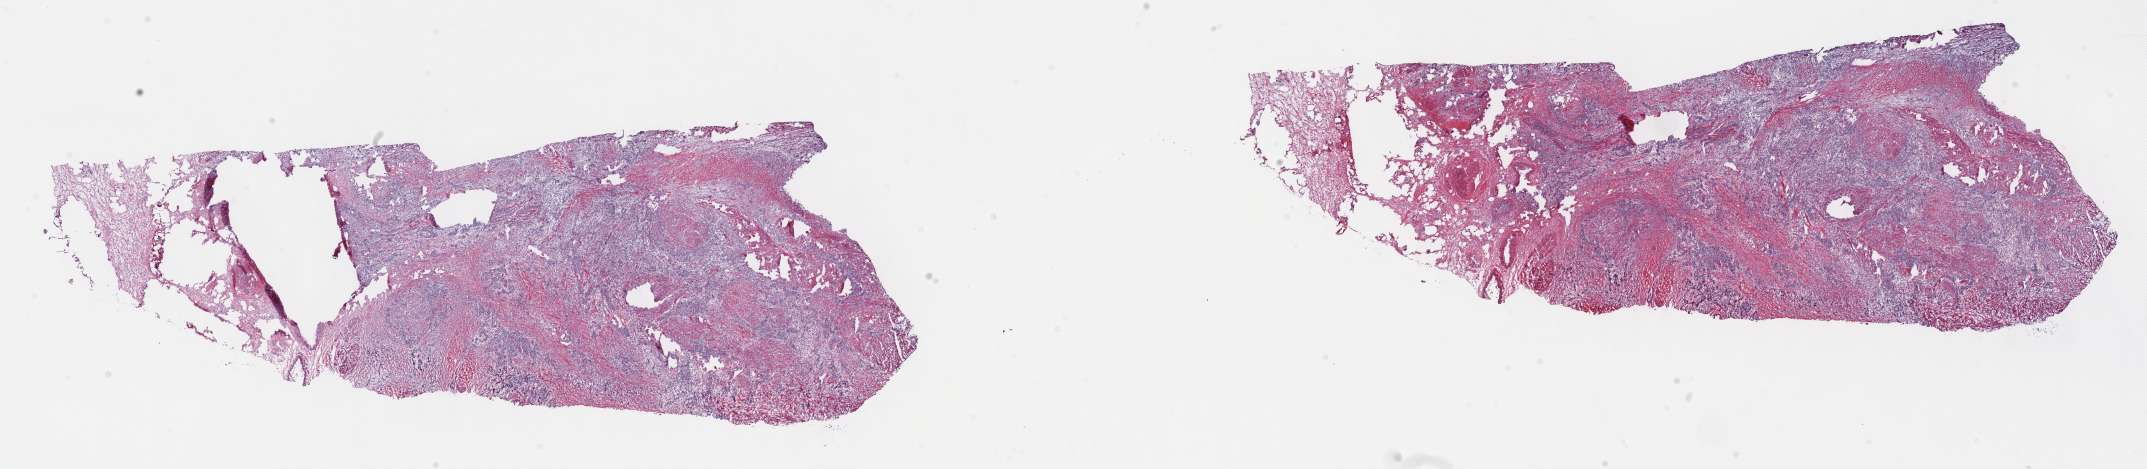
Whole-slide histology image, Hematoxylin and eosin (H&E) stained — shown as a low-resolution overview of the whole scanned area (about 34.7 x 7.6 mm, slide scanned at 40x). Frozen section from the top of the tissue portion. Primary tumour sample from the bladder. Patient: male, age at initial diagnosis 75 years. Histologic grade: high grade. Pathologist review of this section (percent, as recorded): tumour cells 70%, tumour nuclei 70%, normal cells 0%, stromal cells 30%, necrosis 0%. Infiltration values recorded for this section: lymphocyte infiltration 3%, monocyte infiltration 2%, neutrophil infiltration 7%.
AJCC pathologic stage: III (7th edition). Pathologic diagnosis: Transitional cell carcinoma (dome of bladder).